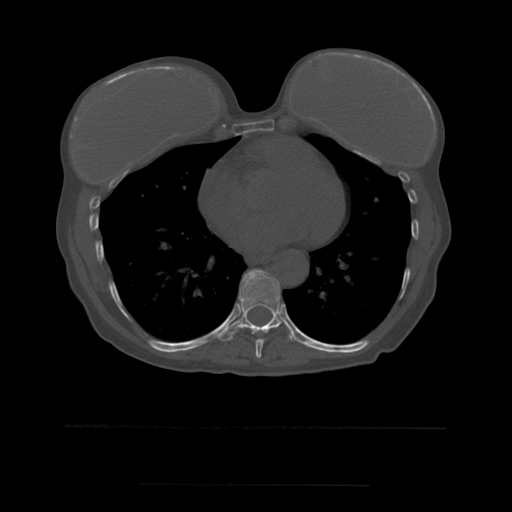
CT including the spine, one axial slice. Slice 328 of 544 in the series (ordered by position). Bone window (W 1800 / L 400 HU). 1.25 mm slice thickness. 512 × 512 image matrix, field of view 350 × 350 mm. Patient age 58 years. From the clinical record (not read from this slice): primary cancer: lung.
Outlined on this slice (semi-automatically segmented with operator editing):
- T8 vertebra: bounding box [x1, y1, x2, y2] px = [251, 328, 273, 359]
- T9 vertebra: [218, 269, 296, 342]